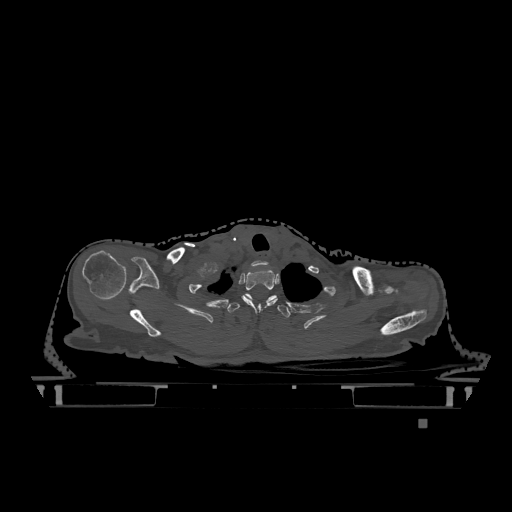
CT including the spine, one axial slice; slice 988 of 1317 in the series (ordered by position); bone window (W 1800 / L 400 HU); 0.5 mm slice thickness; 512 × 512 image matrix, field of view 500 × 500 mm. Patient: female, 74 years. Case-level facts recorded for this patient, not image findings: primary cancer: lung; vertebrae with lytic lesions (as recorded): T1, T4, T5, T6, L4, L5.
Annotated regions visible in this slice (semi-automatic segmentation, software-assisted and operator-edited):
- T1 vertebra: bounding box [x1, y1, x2, y2] px = [241, 269, 277, 312]
- T2 vertebra: [228, 294, 291, 318]